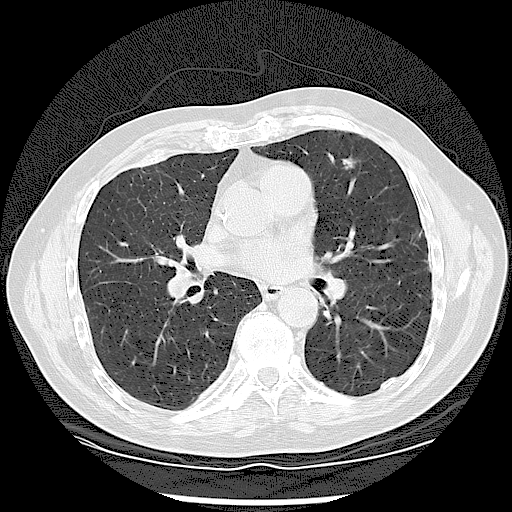
Low-dose screening chest CT, one axial slice. Position 55 of 120 along the scan axis. Reconstruction kernel LUNG. 120 kVp. Lung window (W 1500 / L -600 HU). 512 × 512 image matrix, field of view 360 × 360 mm.
Annotated regions visible in this slice (manually delineated by an expert):
- lesion 1 (tumor, upper lobe of left lung): bounding box [x1, y1, x2, y2] px = [343, 158, 355, 169]